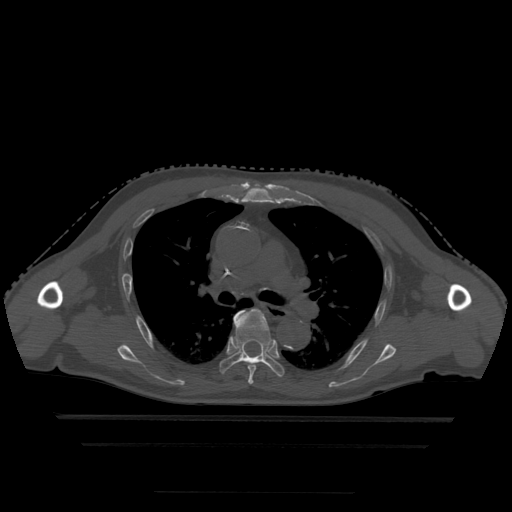
CT including the spine, one axial slice; slice 324 of 522 in the series (ordered by position); bone window (W 1800 / L 400 HU); 1.25 mm slice thickness; 512 × 512 image matrix, field of view 436 × 436 mm. Patient age 68 years. From the clinical record (not read from this slice): primary cancer: urothelial.
Outlined on this slice (semi-automatically segmented with operator editing):
- T5 vertebra: bounding box <235,309,261,385> (left, top, right, bottom; pixels)
- T6 vertebra: <219,310,284,377>